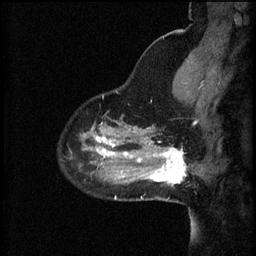
Breast MRI (dynamic contrast-enhanced), one sagittal slice. Slice 15 of 60 in the series (ordered by position). 3 images stored at this slice position (order not interpretable as contrast timing). 1.5 T. TE 4.2 ms, TR 8.2 ms. 2 mm slice thickness. 256 × 256 image matrix. Female patient, age 37 years.
Outlined on this slice (semi-automatic segmentation, software-assisted and operator-edited):
- analysis volume of interest (the breast-tissue region the enhancement analysis was run in; not a lesion): box from (x=148, y=140) to (x=189, y=187) px
- tumour enhancement mask (voxels above the 70 % enhancement threshold inside the analysis volume of interest): (x=148, y=142)–(x=187, y=185)